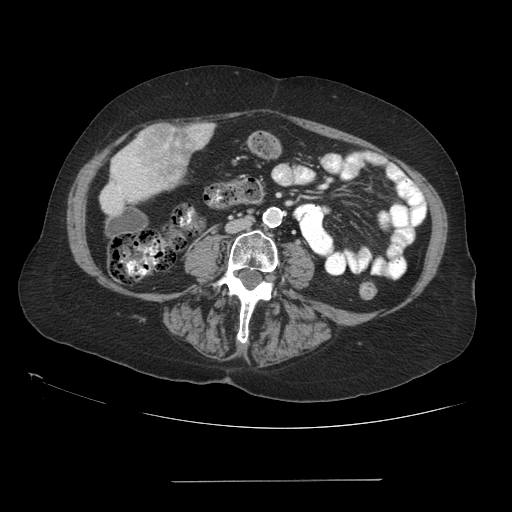
Contrast-enhanced abdominal CT (liver protocol), one axial slice; position 16 of 89 along the scan axis; 140 kVp; soft-tissue window (W 400 / L 40 HU); 512 × 512 image matrix. From the clinical record (not read from this slice): diagnosis: hepatocellular carcinoma (patient treated with transarterial chemoembolisation; whether this scan precedes or follows treatment is not stated here); TNM stage (as recorded): Stage-IVA; Child-Pugh class: A; tumour nodularity: uninodular.
Annotated regions visible in this slice (semi-automatic segmentation, software-assisted and operator-edited):
- liver parenchyma outside the tumour (the mass and vessels are separate outlines, so this box may not span the whole liver): box from (x=102, y=202) to (x=118, y=214) px
- mass: (x=127, y=122)–(x=215, y=185)